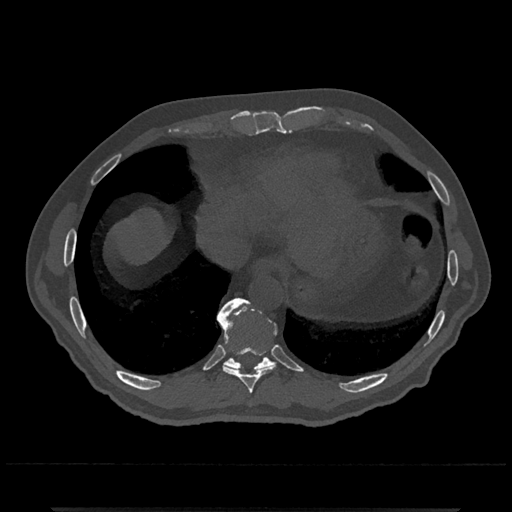
CT including the spine, one axial slice; slice 590 of 797 in the series (ordered by position); reconstruction kernel Br40s/3; 120 kVp; bone window (W 1800 / L 400 HU); 512 × 512 image matrix, field of view 393 × 393 mm. Male patient, age 67 years. From the clinical record (not read from this slice): primary cancer: prostate.
Structures marked on this image (semi-automatically segmented with operator editing):
- T10 vertebra: box from (x=218, y=298) to (x=276, y=372) px
- T9 vertebra: (x=217, y=302)–(x=277, y=394)